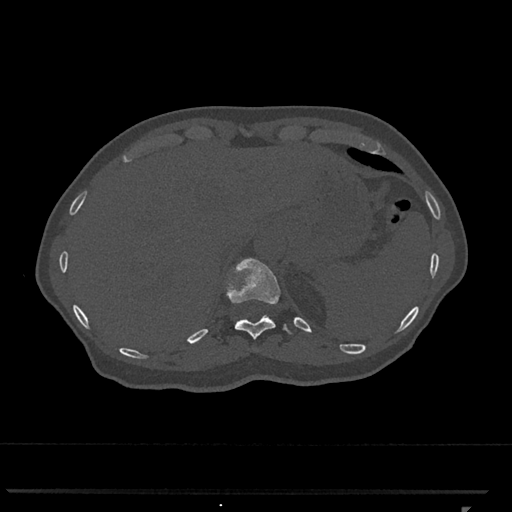
CT including the spine, one axial slice. Position 511 of 793 along the scan axis. 120 kVp. Bone window (W 1800 / L 400 HU). 0.5 mm slice thickness. 512 × 512 image matrix, field of view 380 × 380 mm. Patient: female, 62 years. From the clinical record (not read from this slice): primary cancer: renal.
Structures marked on this image (semi-automatic segmentation, software-assisted and operator-edited):
- T11 vertebra: bounding box [x1, y1, x2, y2] px = [226, 258, 291, 339]